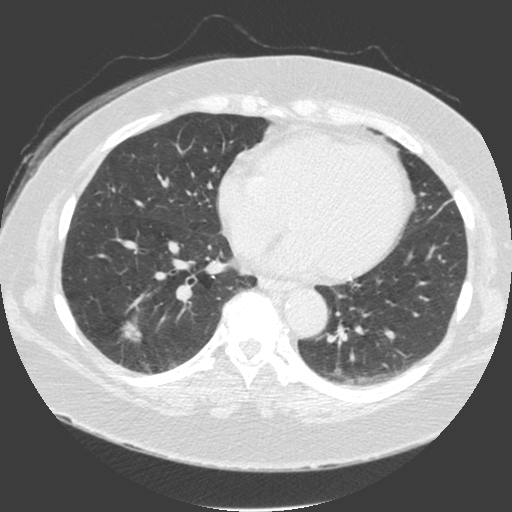
Low-dose screening chest CT, one axial slice. Position 72 of 175 along the scan axis. Lung window (W 1500 / L -600 HU). 2 mm slice thickness. 512 × 512 image matrix, field of view 370 × 370 mm.
Annotated regions visible in this slice (expert manual segmentation):
- lesion 1 (tumor, lower lobe of right lung): bounding box <124,323,141,340> (left, top, right, bottom; pixels)